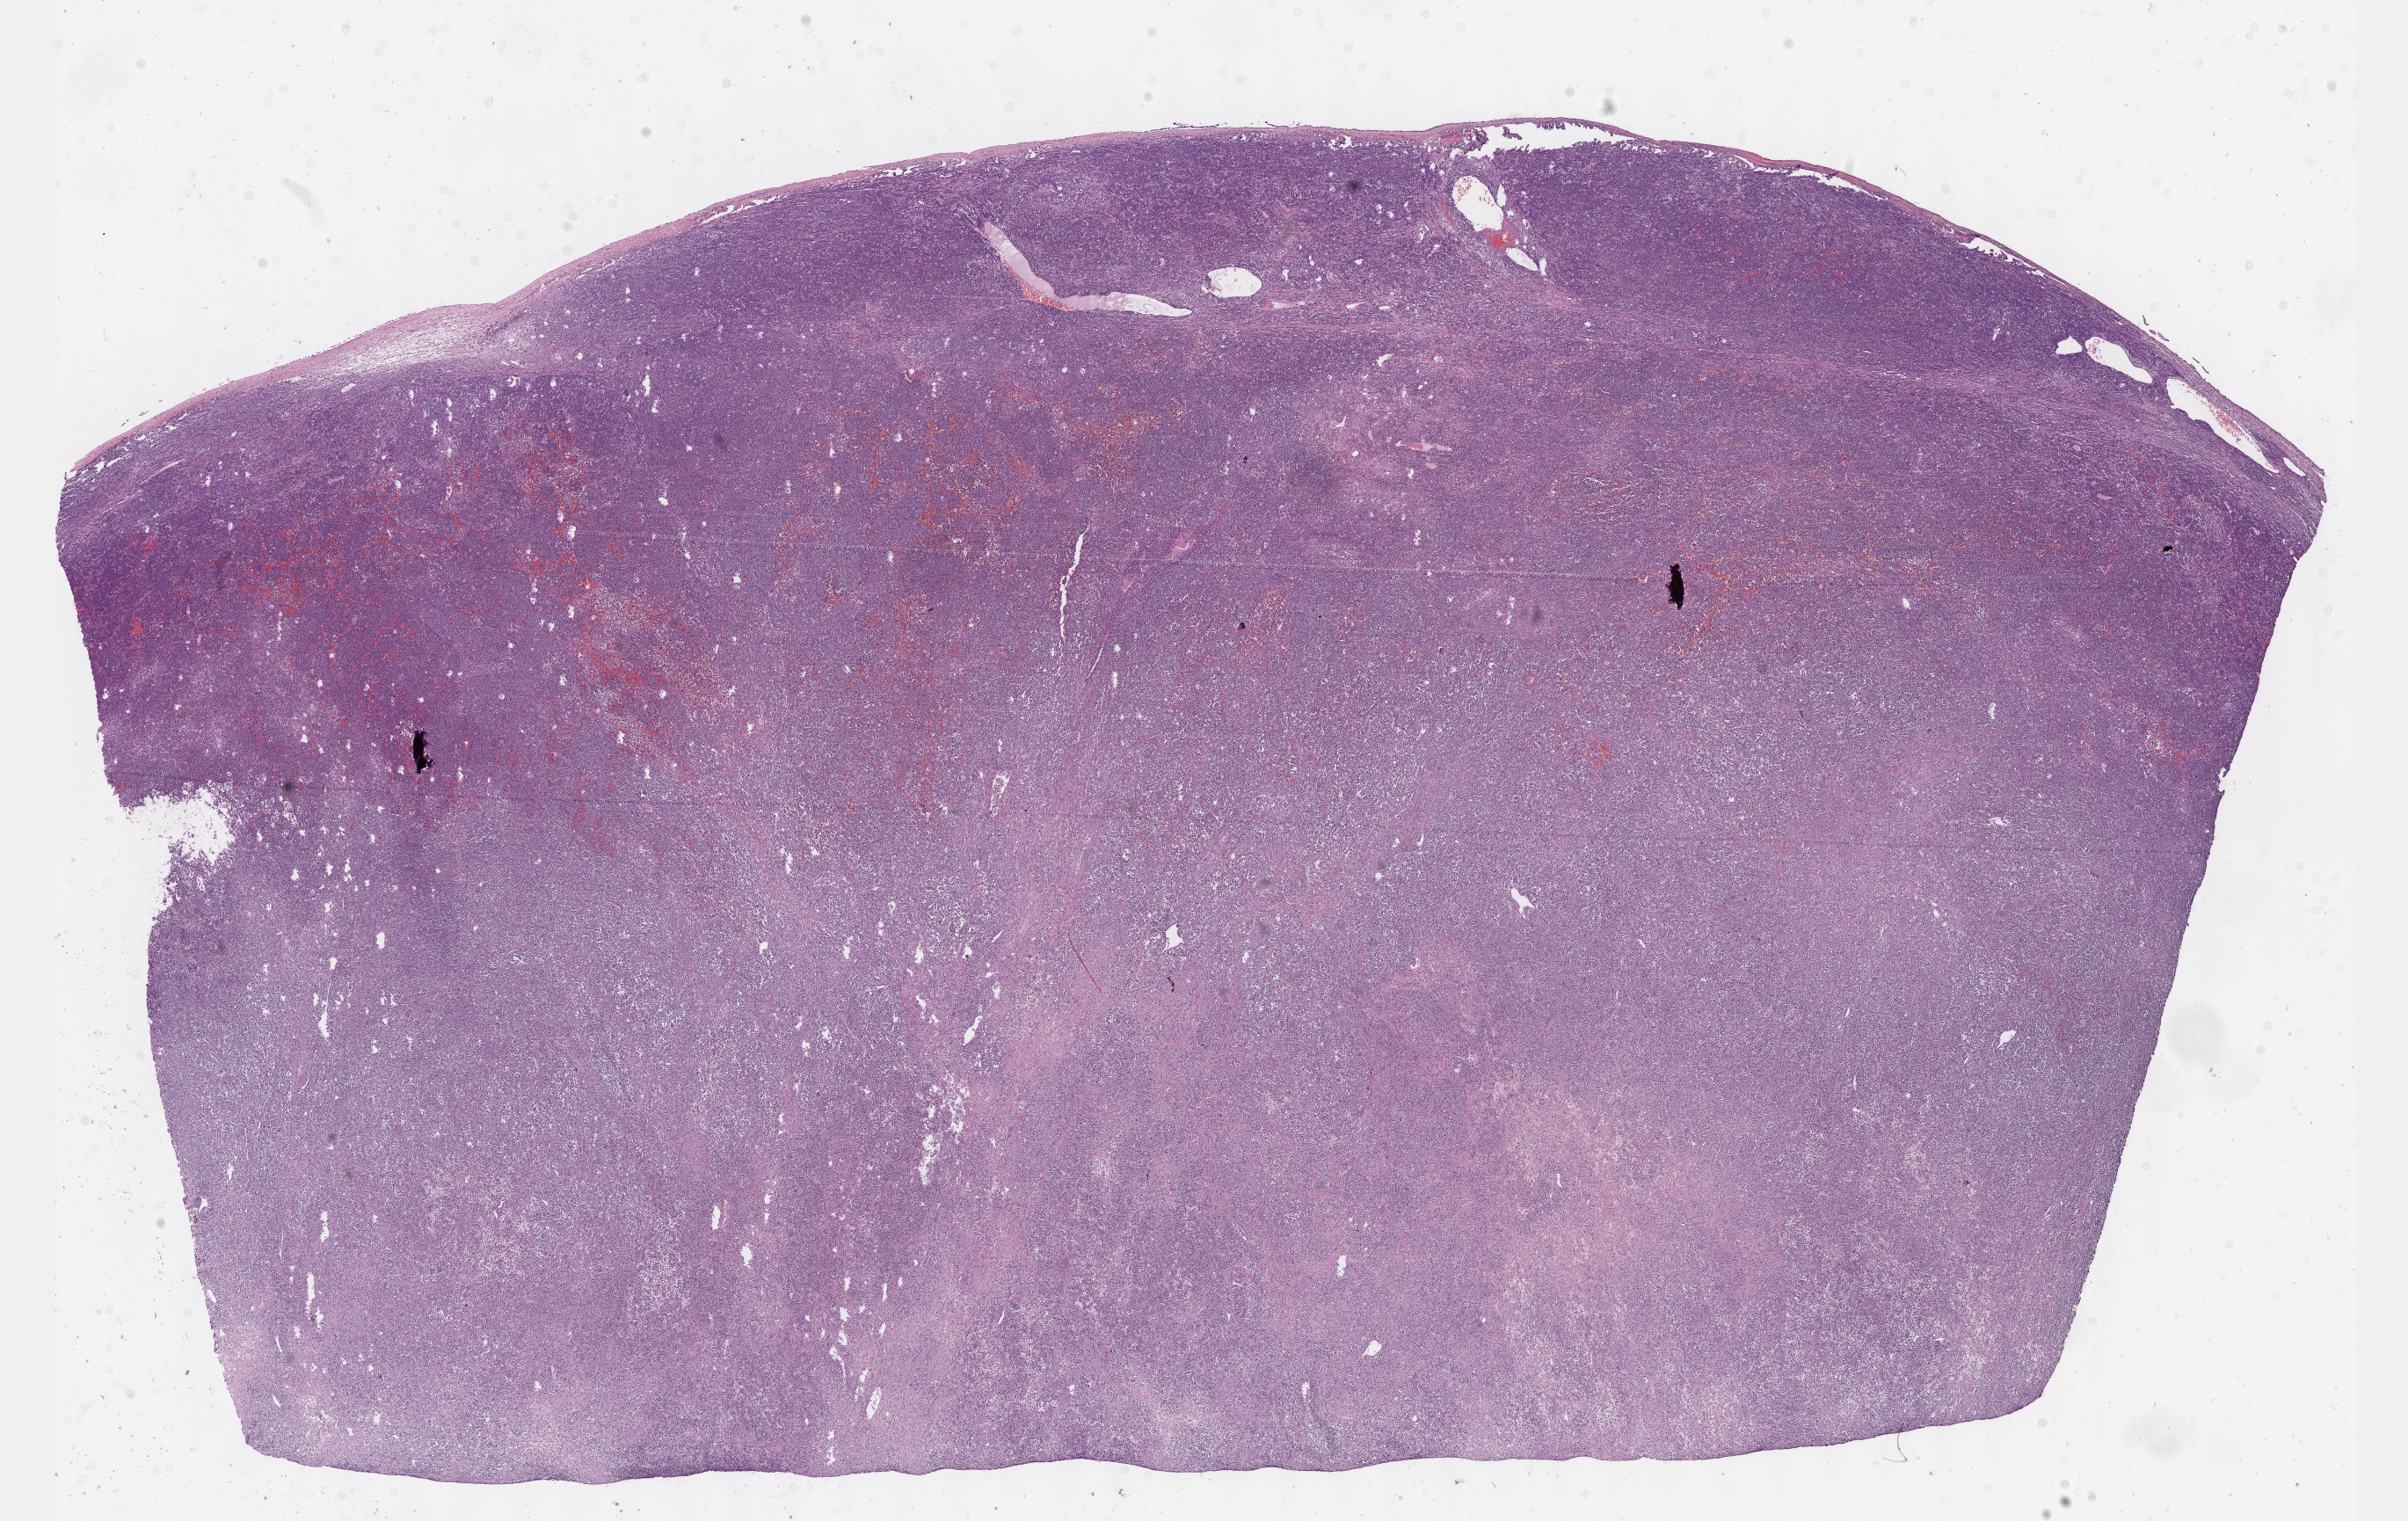
Hematoxylin and eosin (H&E) stained whole-slide image — shown as a low-resolution overview of the whole scanned area (about 22.1 x 14.0 mm, slide scanned at 40x); FFPE section; sample: primary tumour, lymphoid tissue. Male patient; age at initial diagnosis 70 years.
* diagnosis: Diffuse large B-cell lymphoma, NOS (testis, NOS)